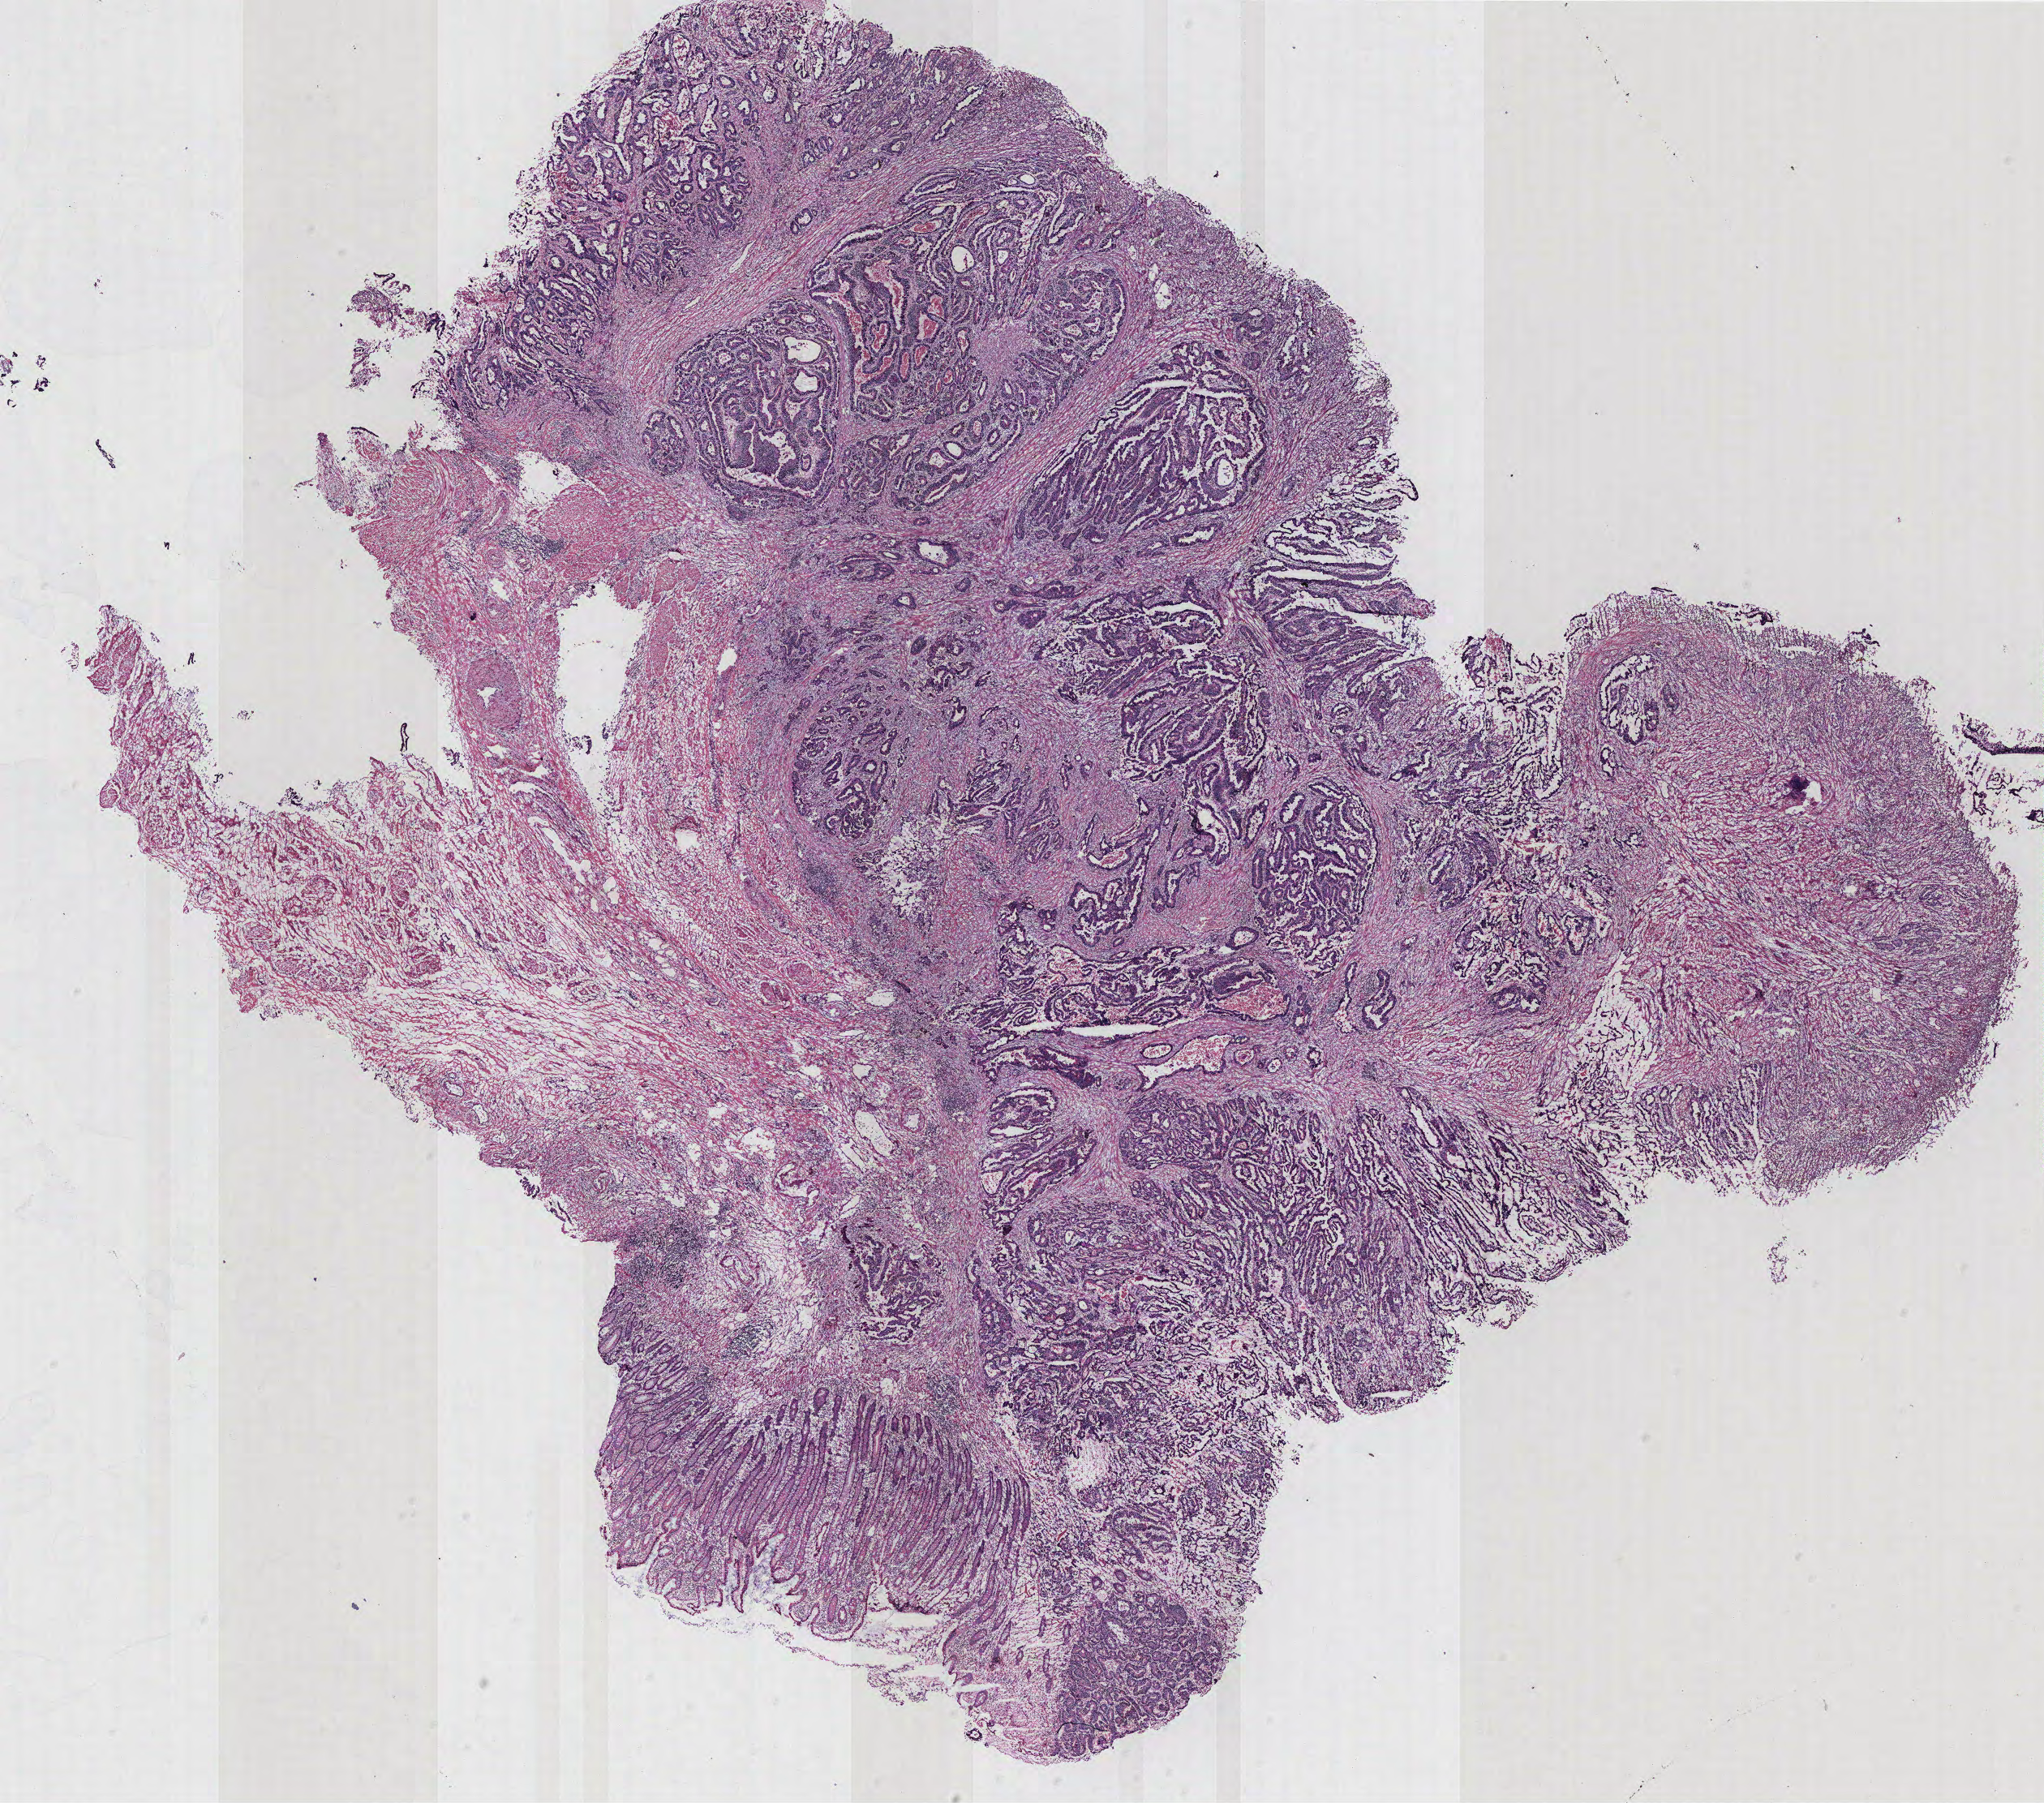
Whole-slide histology image, Hematoxylin and eosin (H&E) stained, low-resolution overview of the scanned area, about 20.2 x 17.8 mm (acquisition: 40x scan); normal (non-tumour) tissue sample, colon. 59-year-old male patient.
* this section: normal (non-tumour) tissue from the same patient
* patient diagnosis: Adenocarcinoma, NOS